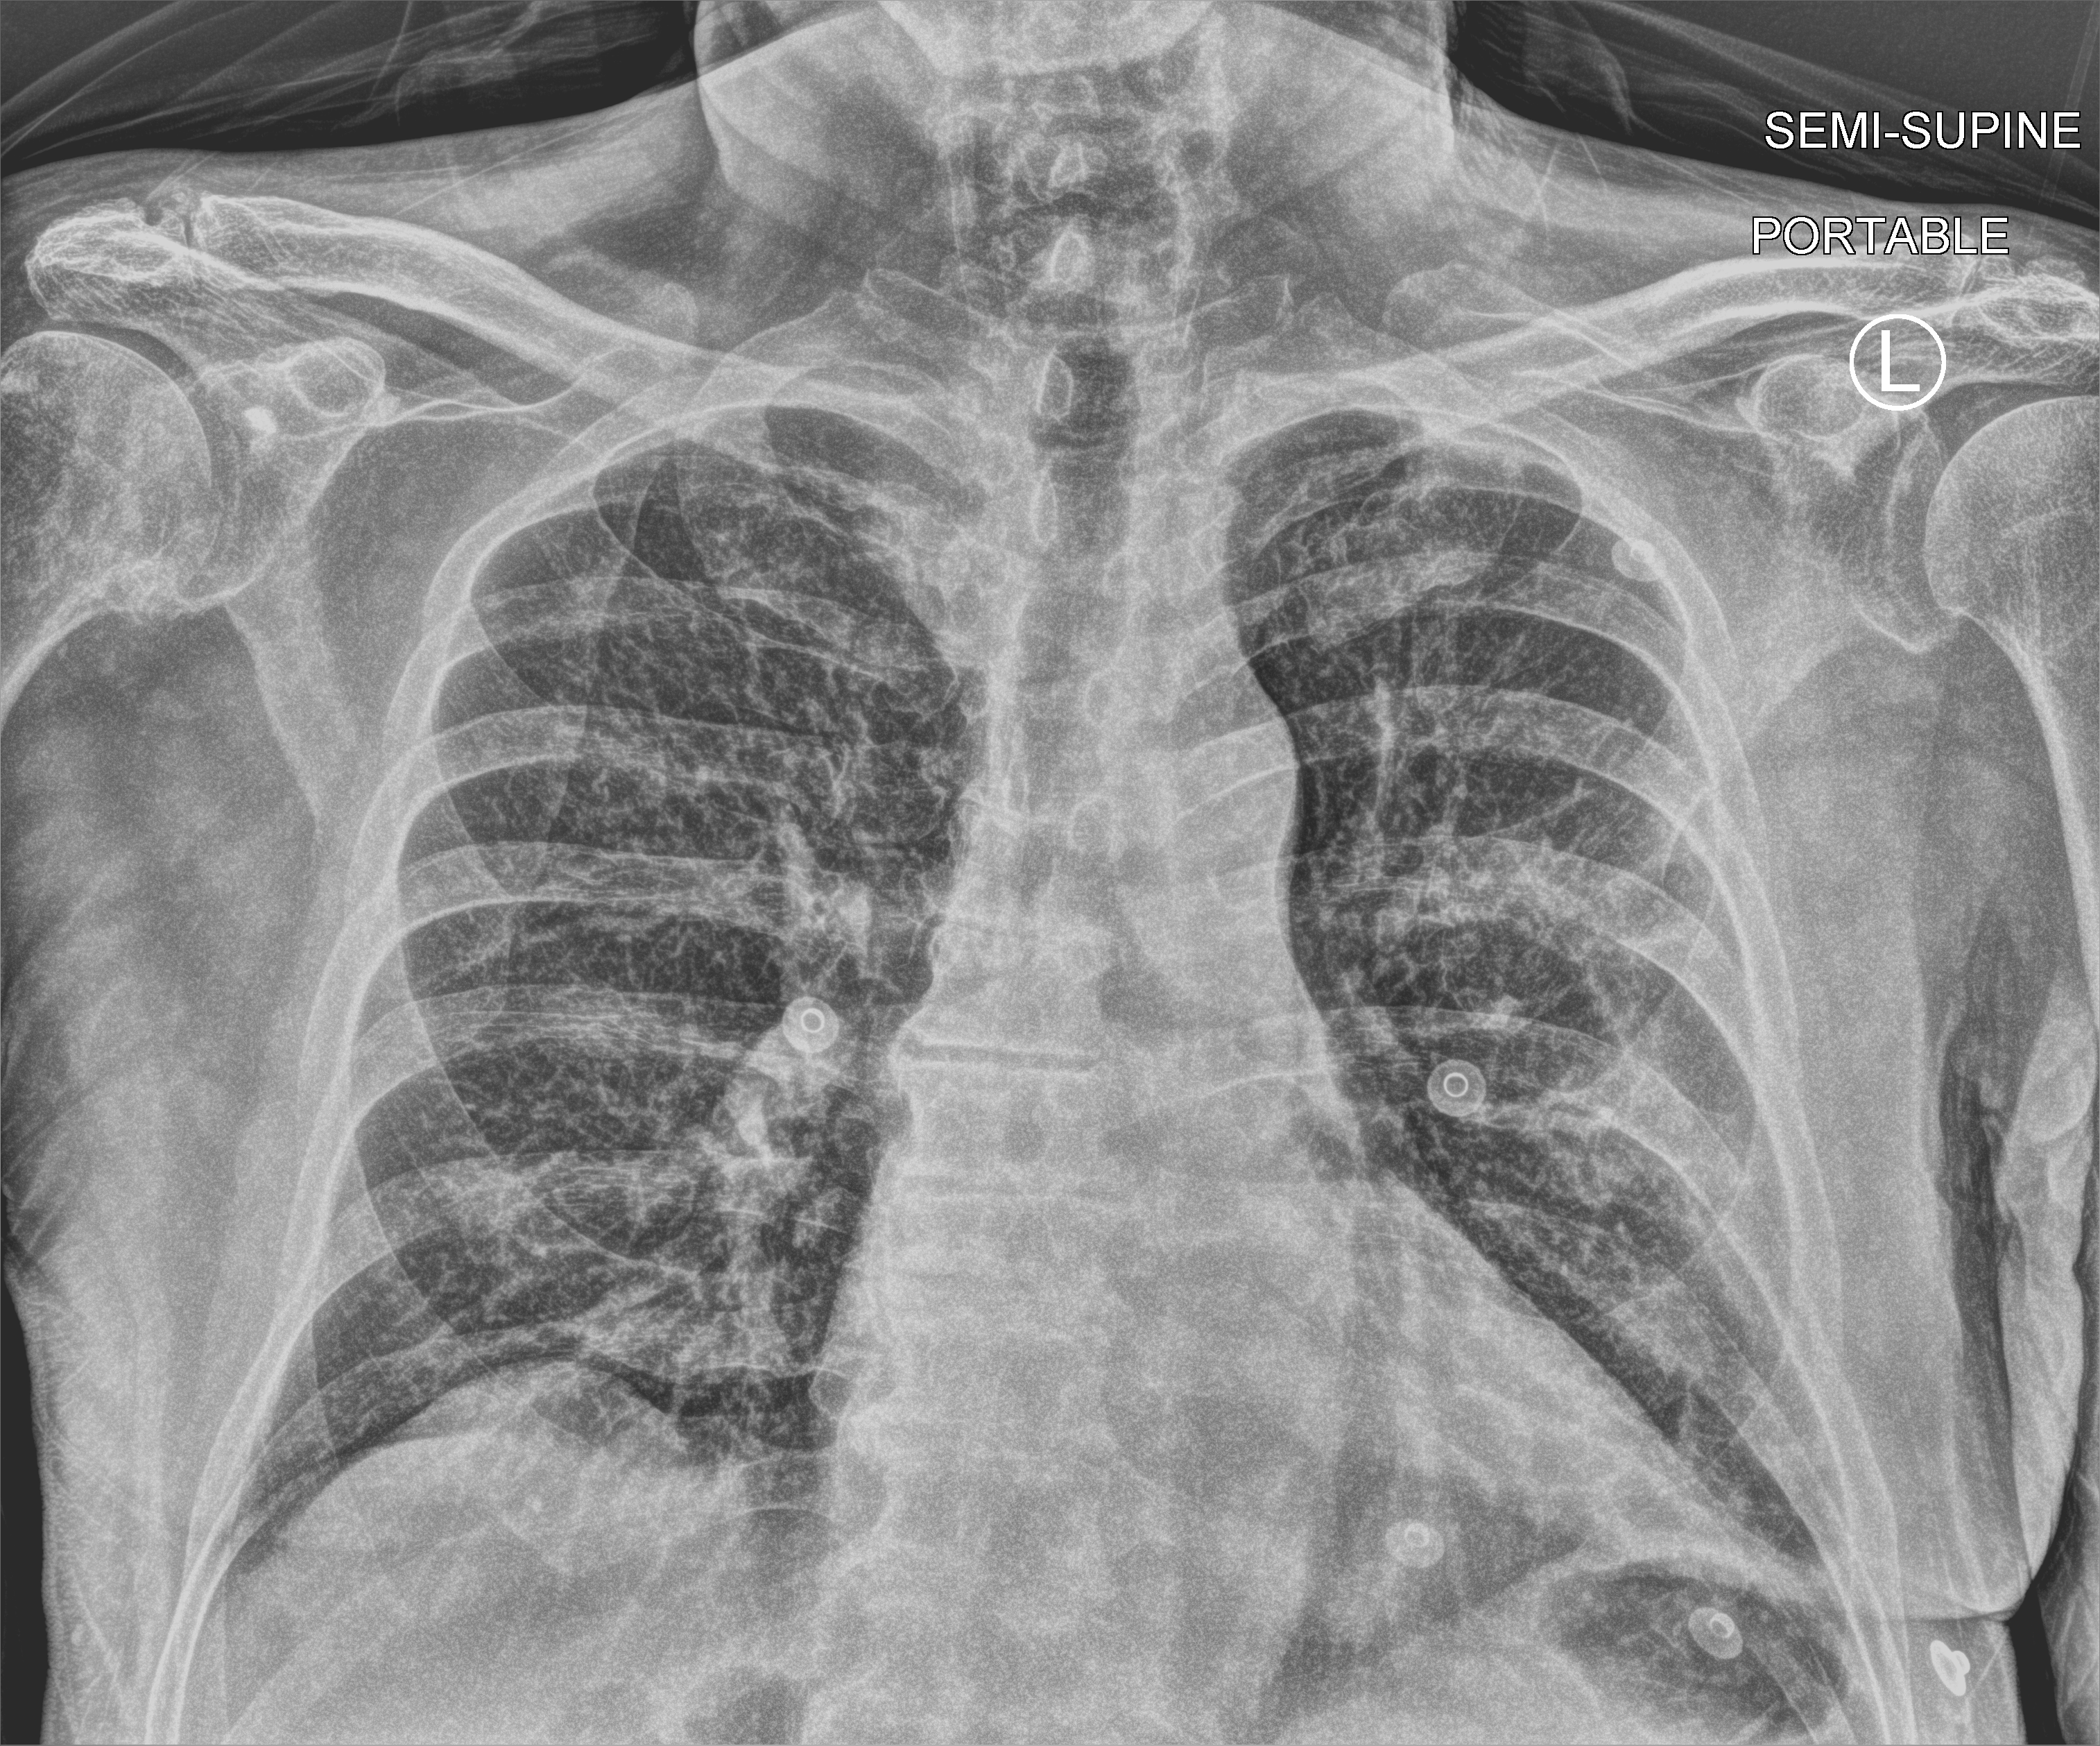
Portable chest radiograph, anteroposterior (AP) projection. Patient hospitalised with COVID-19; male, aged 75–90 years.
From the hospital-stay record, not from the radiograph (when in the stay this image was taken is not recorded): admitted to intensive care during this hospital stay: no; other chronic lung disease (admission record): yes.